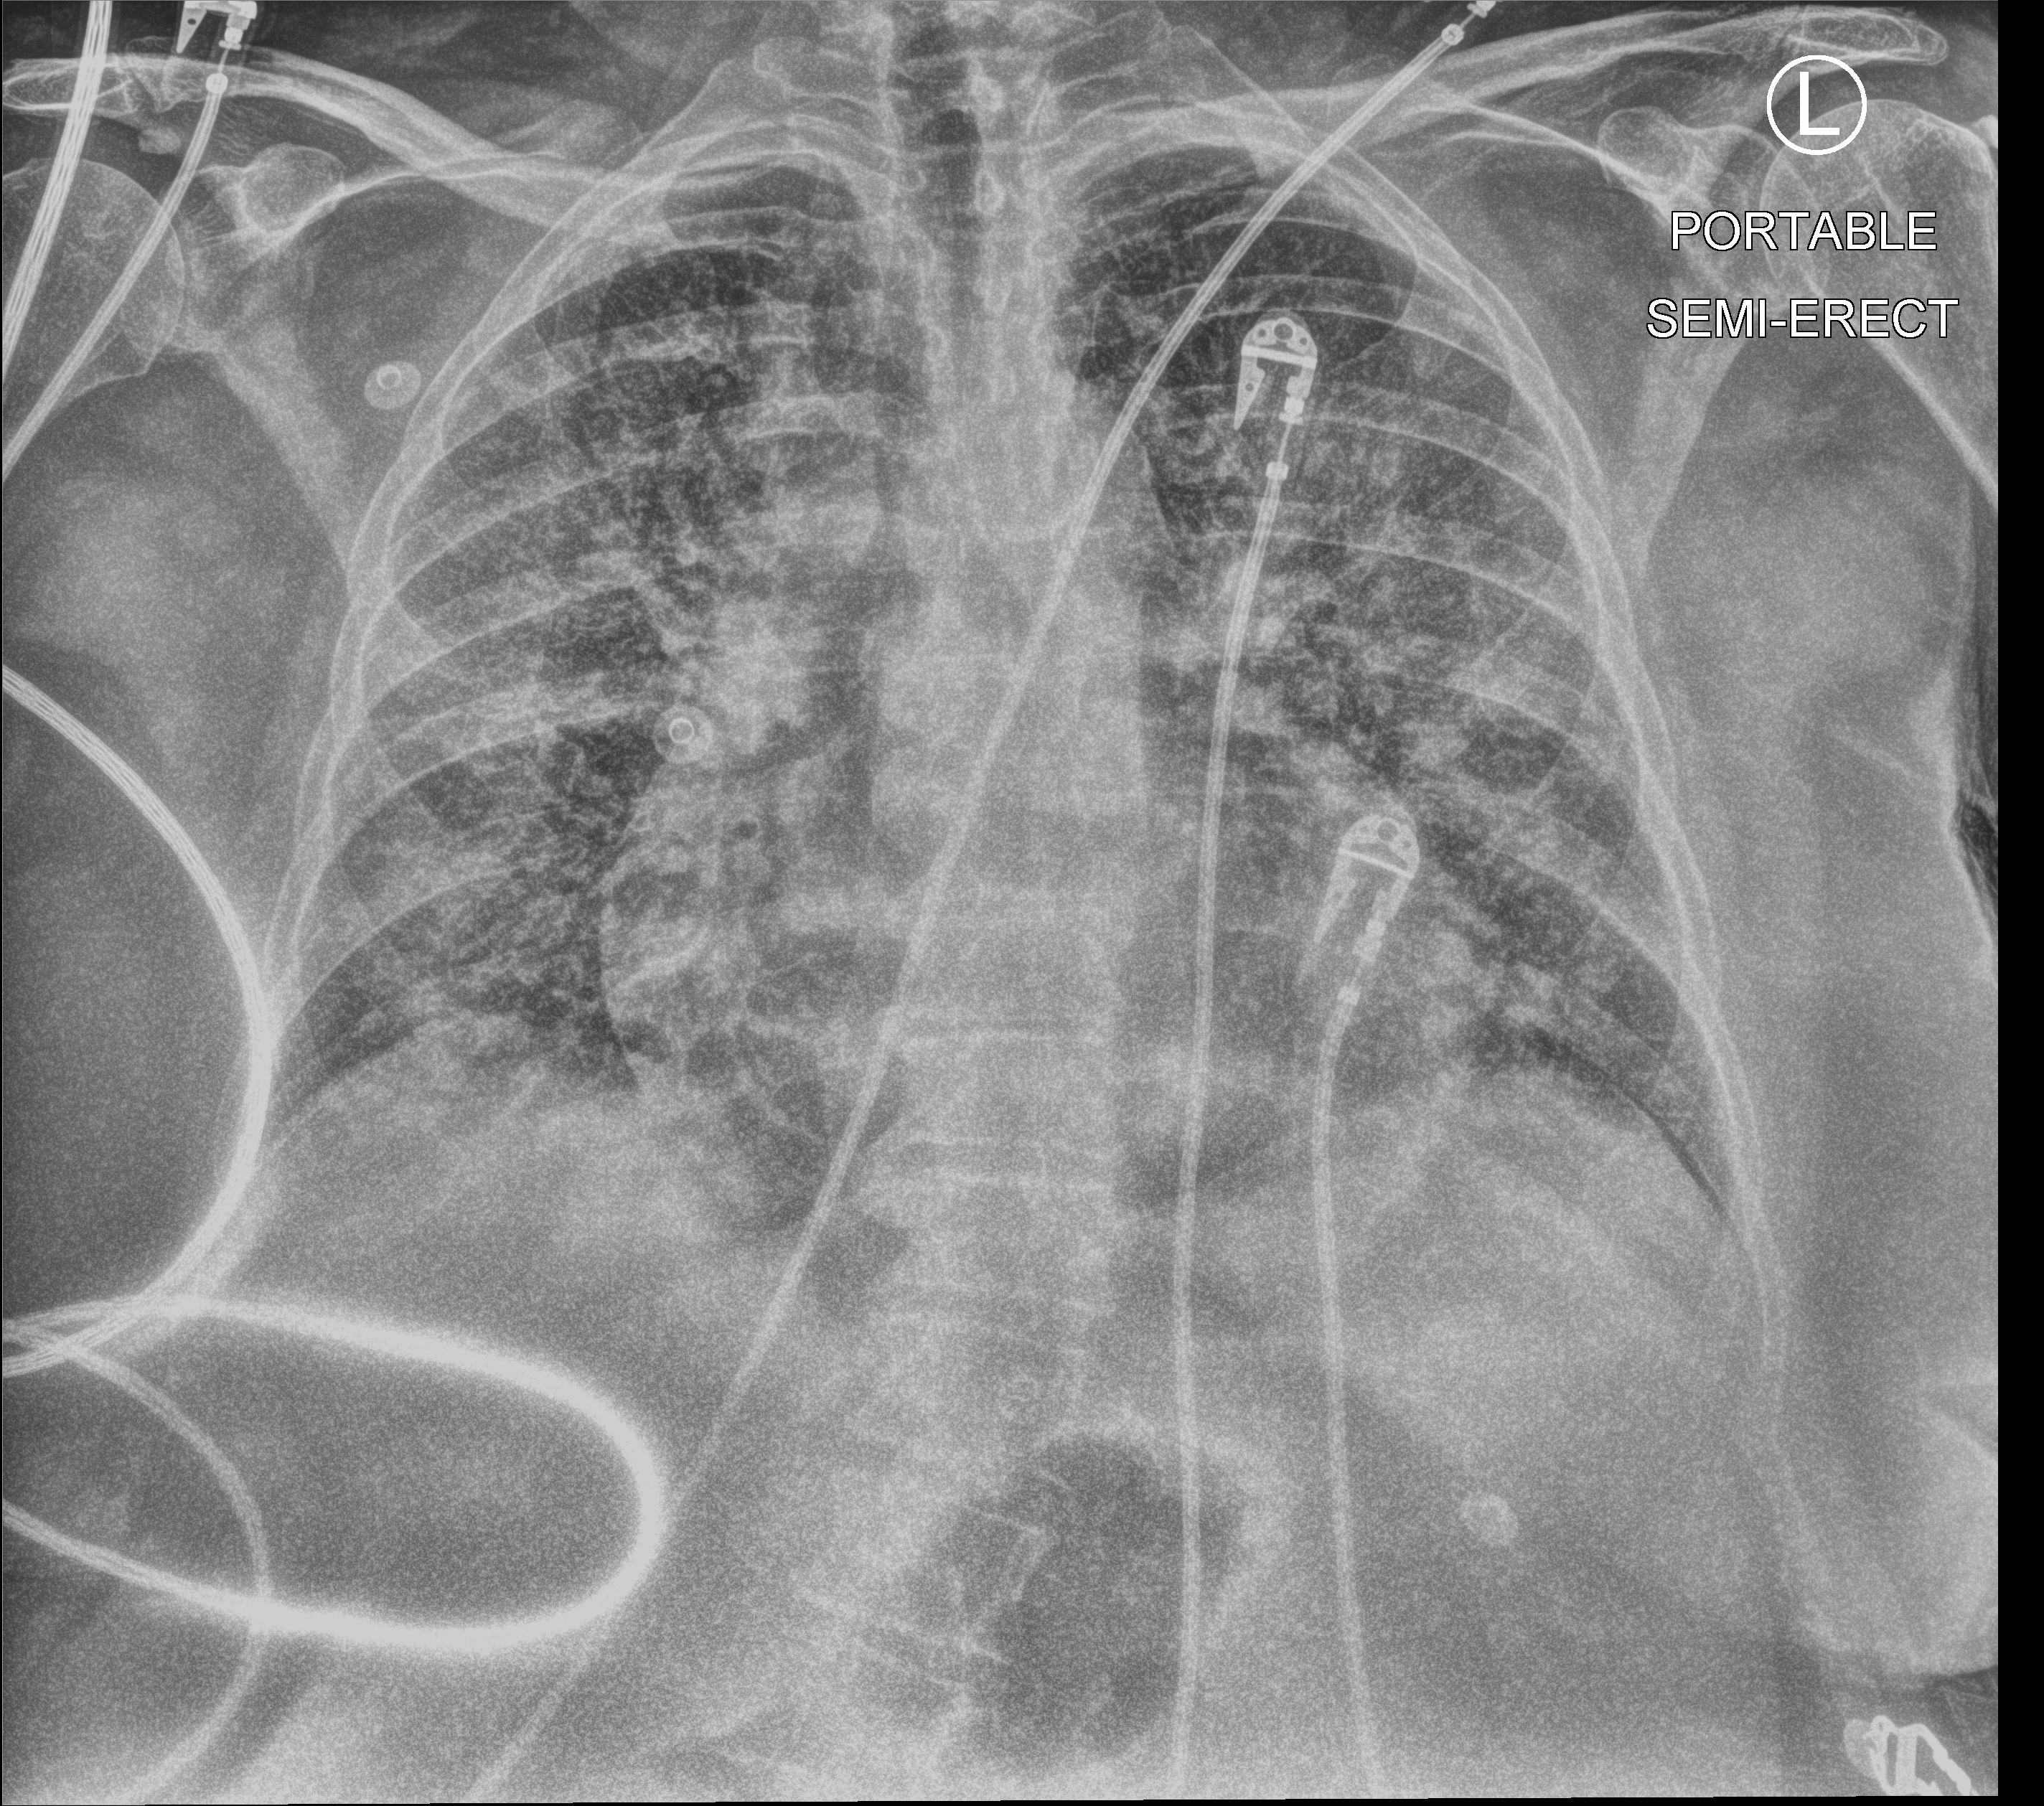
Portable chest radiograph, anteroposterior (AP) projection. Patient hospitalised with COVID-19; female, aged 75–90 years.
Admission-level facts for this patient (not findings on this image; timing relative to this image not recorded): hypertension (admission record): yes; other chronic lung disease (admission record): yes; admitted to intensive care during this hospital stay: yes.